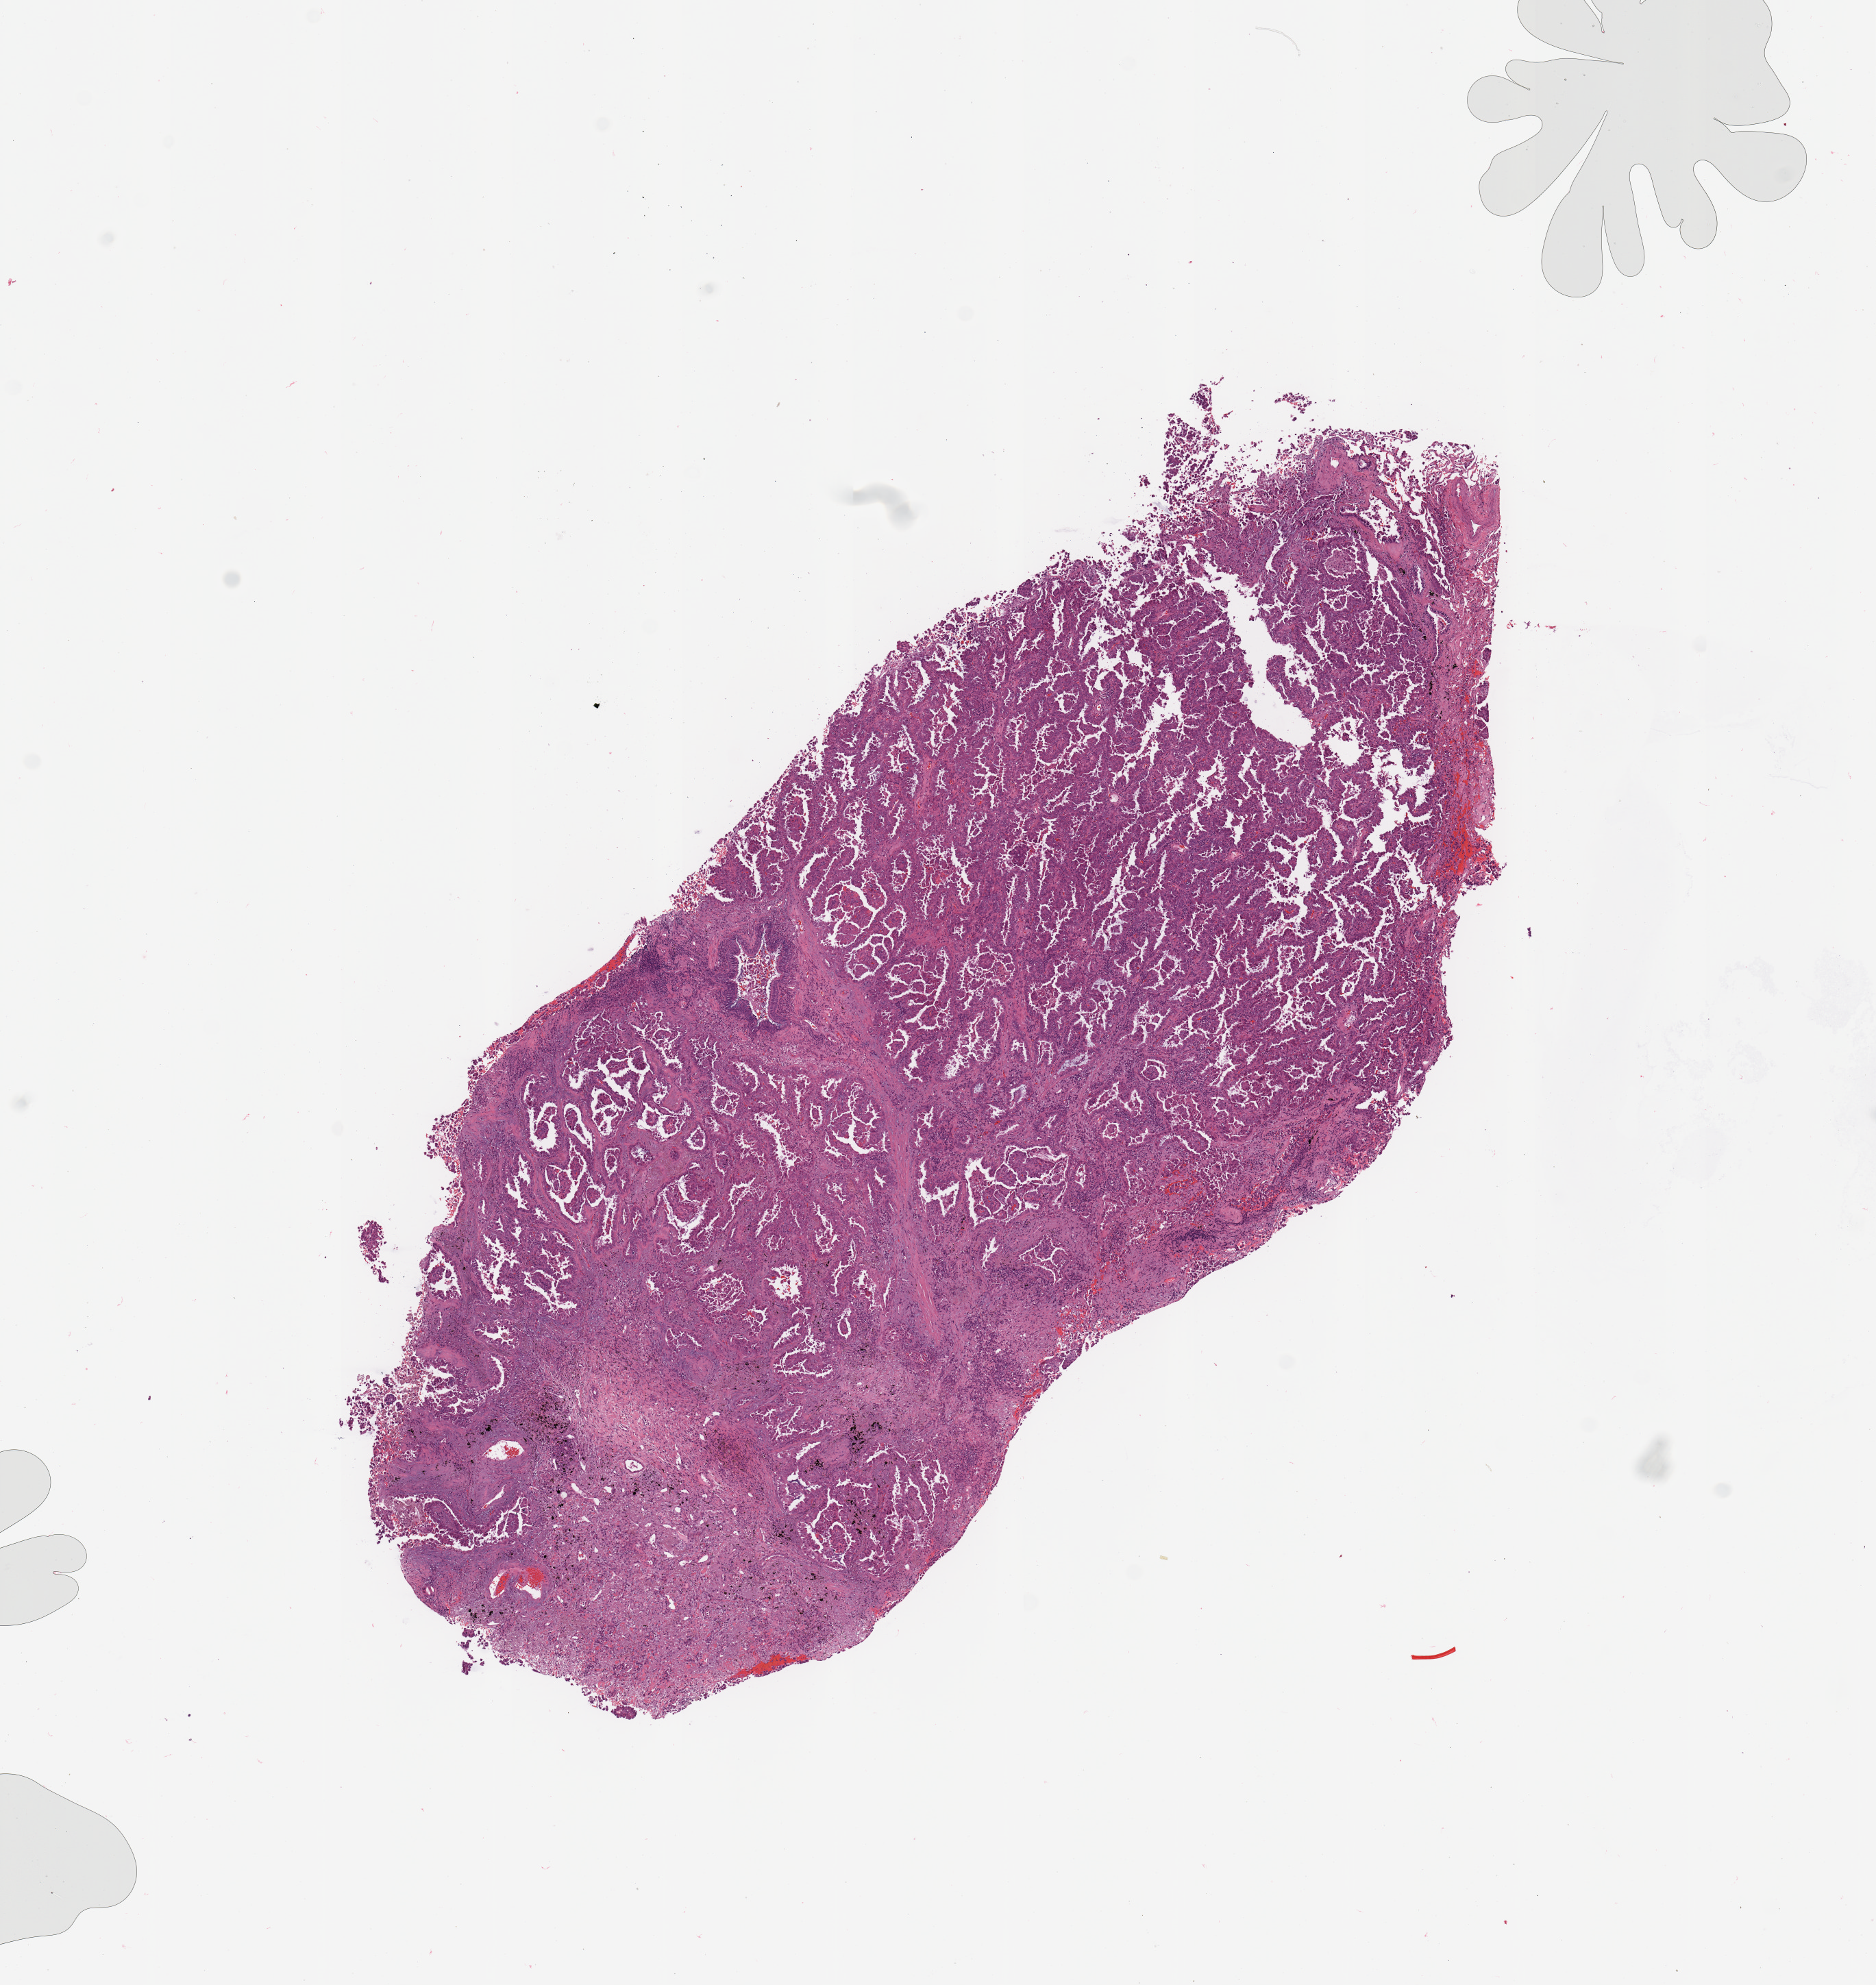
Whole-slide histology image, Hematoxylin and eosin (H&E) stained, shown as a low-resolution overview of the whole scanned area (about 10.8 x 11.5 mm, slide scanned at 20x). Tumour tissue sample, sampled site: lung. Patient: male, age 77 years. Histologic grade: G2 (moderately differentiated). Composition of this section per pathologist review: tumour nuclei 75%, necrosis 0%.
Histologic diagnosis: Adenocarcinoma, NOS. AJCC pathologic stage: IIA.